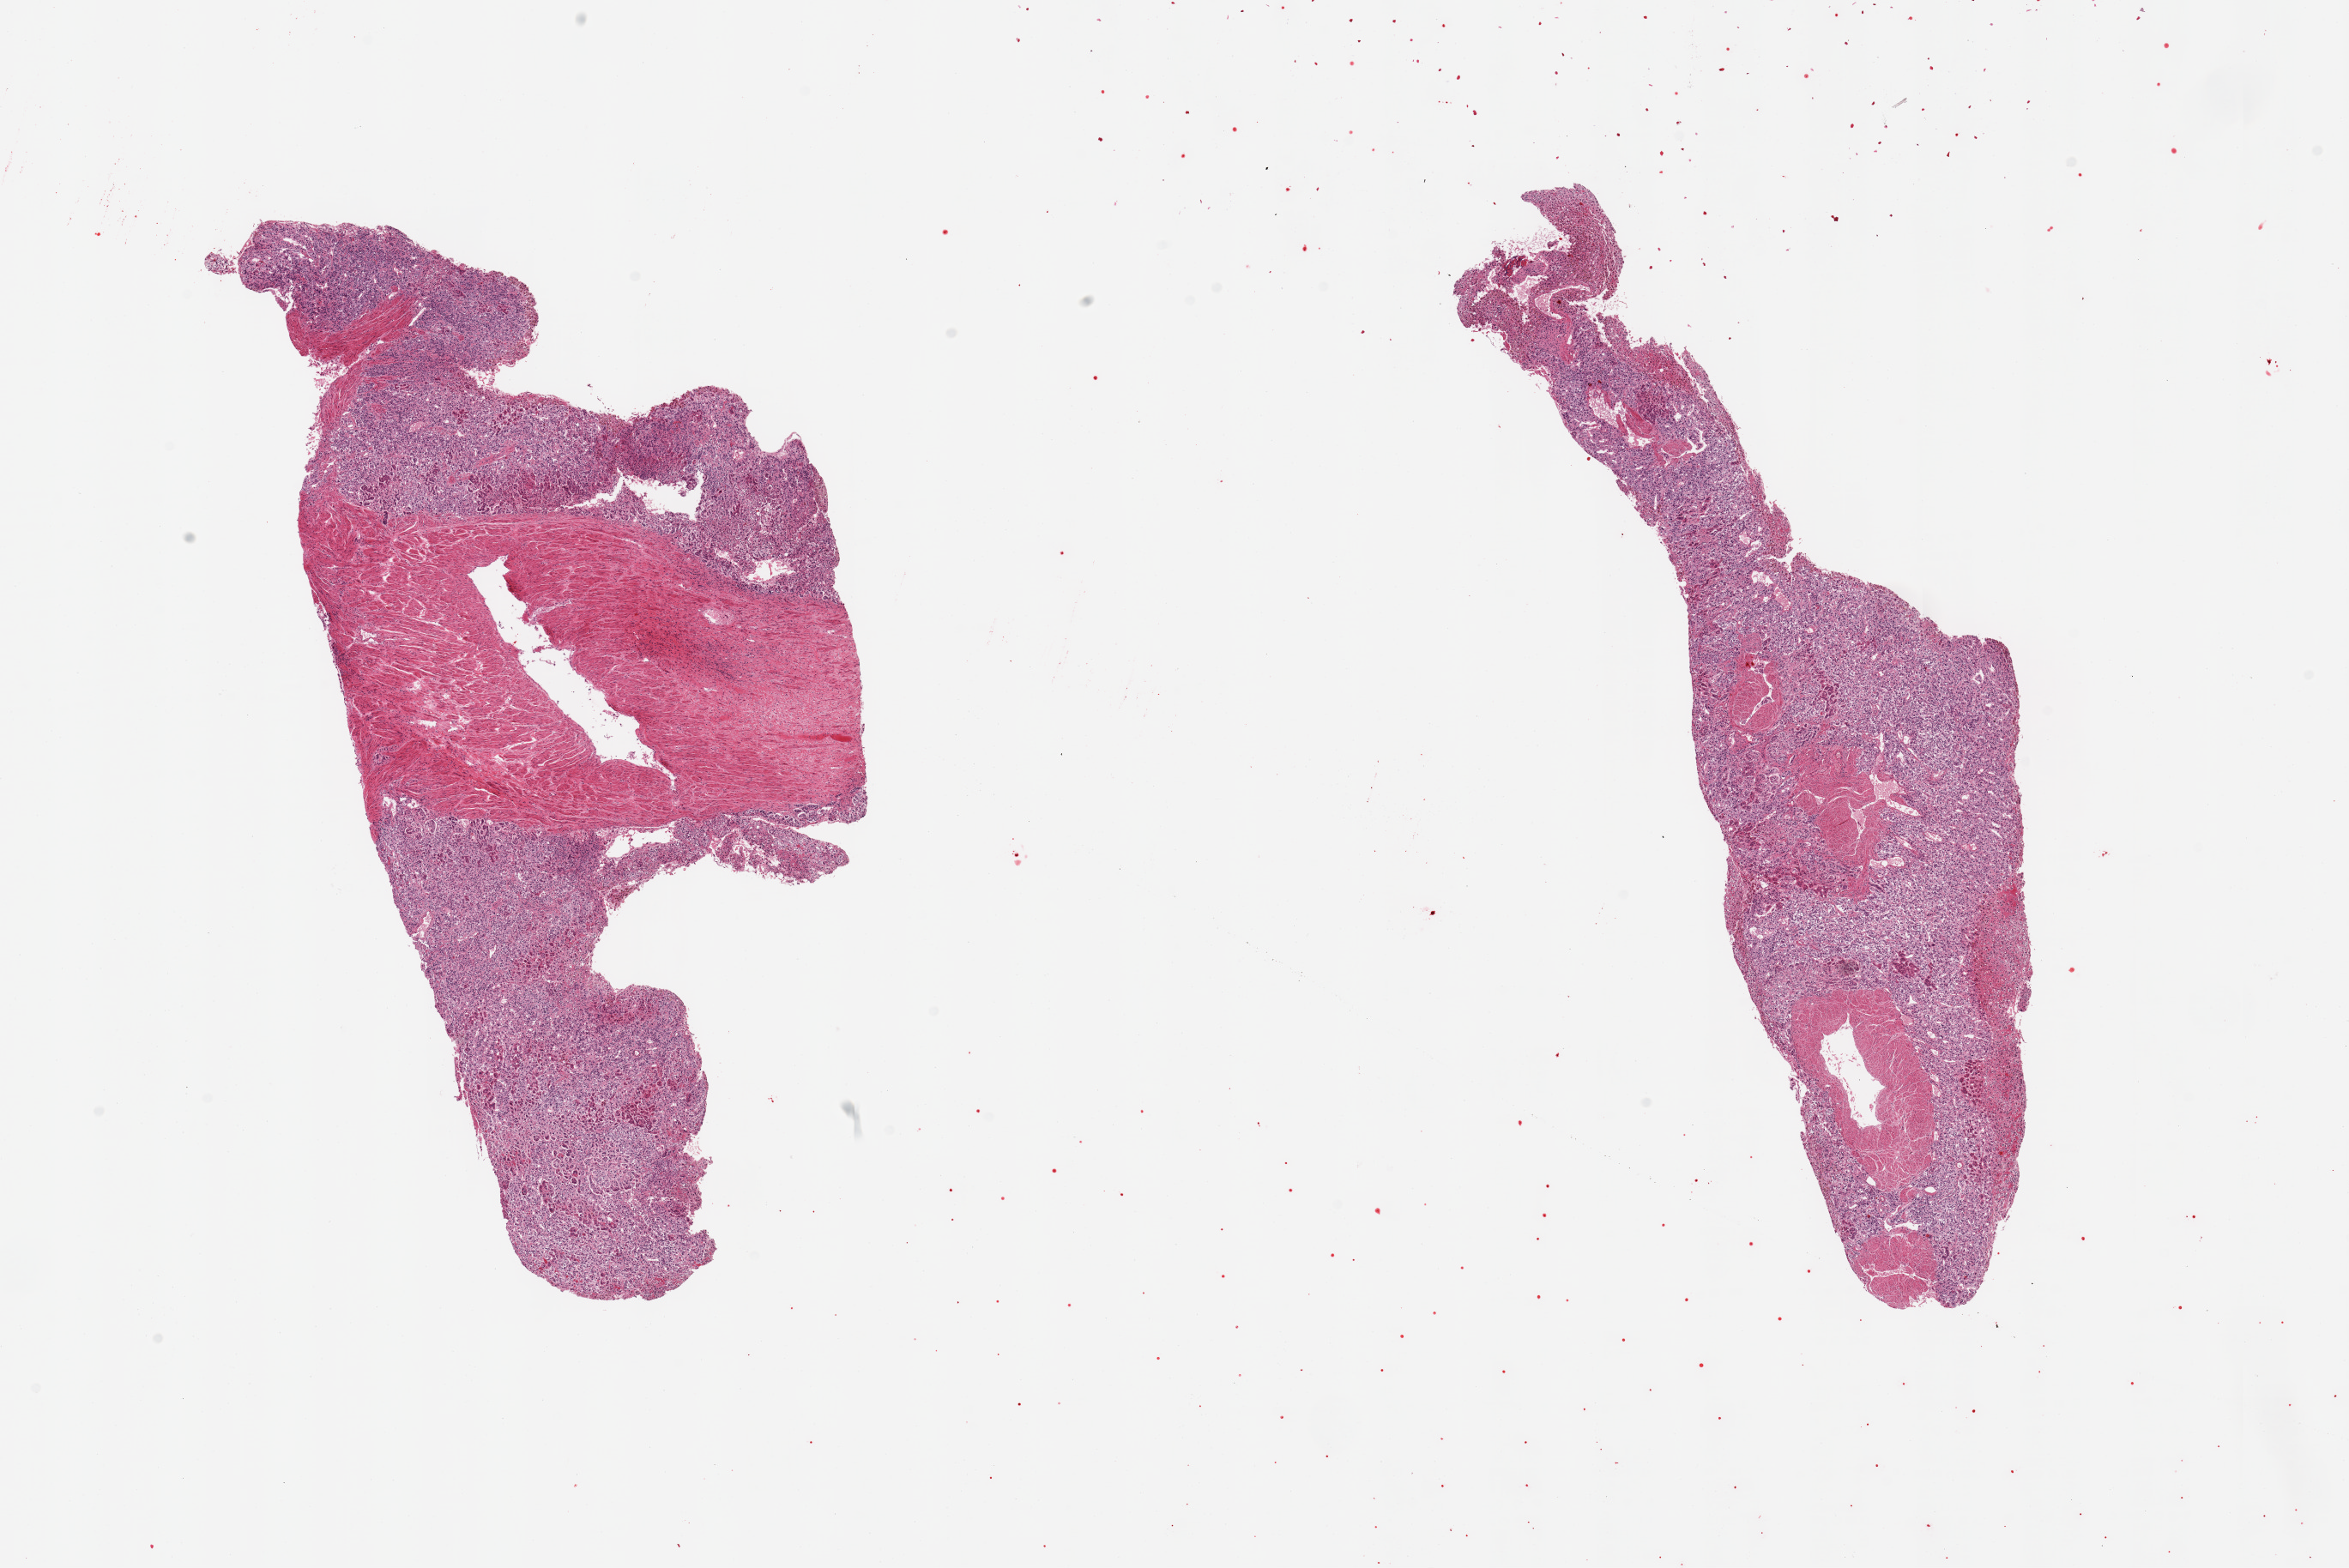
Whole-slide image, hematoxylin and eosin (H&E) stain, brightfield, whole scanned area (about 21.7 x 14.5 mm, acquisition: 20x scan) shown as a low-resolution overview, PAXgene-fixed paraffin-embedded (PFPE) section, target tissue: adrenal gland, tissue donor sample. Donor: male.
Review note (as recorded): 2 pieces; large blood vessel occupies 60% of 1 piece & 30% of other.